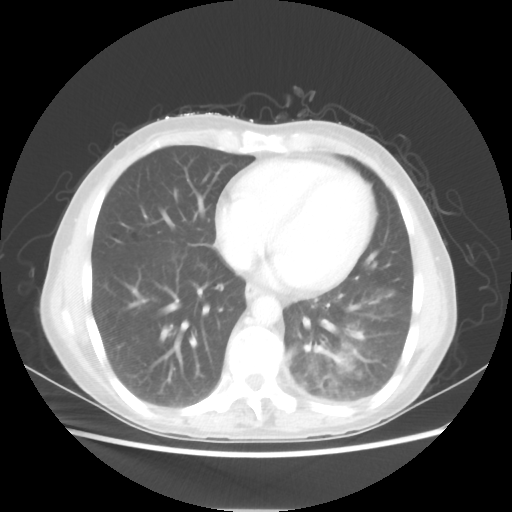
Chest CT, one axial slice. Slice 21 of 56 in the series (ordered by position). Reconstruction kernel STANDARD. 80 kVp. Lung window (W 1500 / L -600 HU). 5 mm slice thickness. 512 × 512 image matrix, field of view 360 × 360 mm. Female patient, age 53 years. From the clinical record (not read from this slice): clinical TNM (as recorded): T3 N0 M0.
Annotated regions visible in this slice (rectangle marked by the reading radiologist):
- lung tumour (recorded histology: adenocarcinoma): bounding box <321,349,336,359> (left, top, right, bottom; pixels)